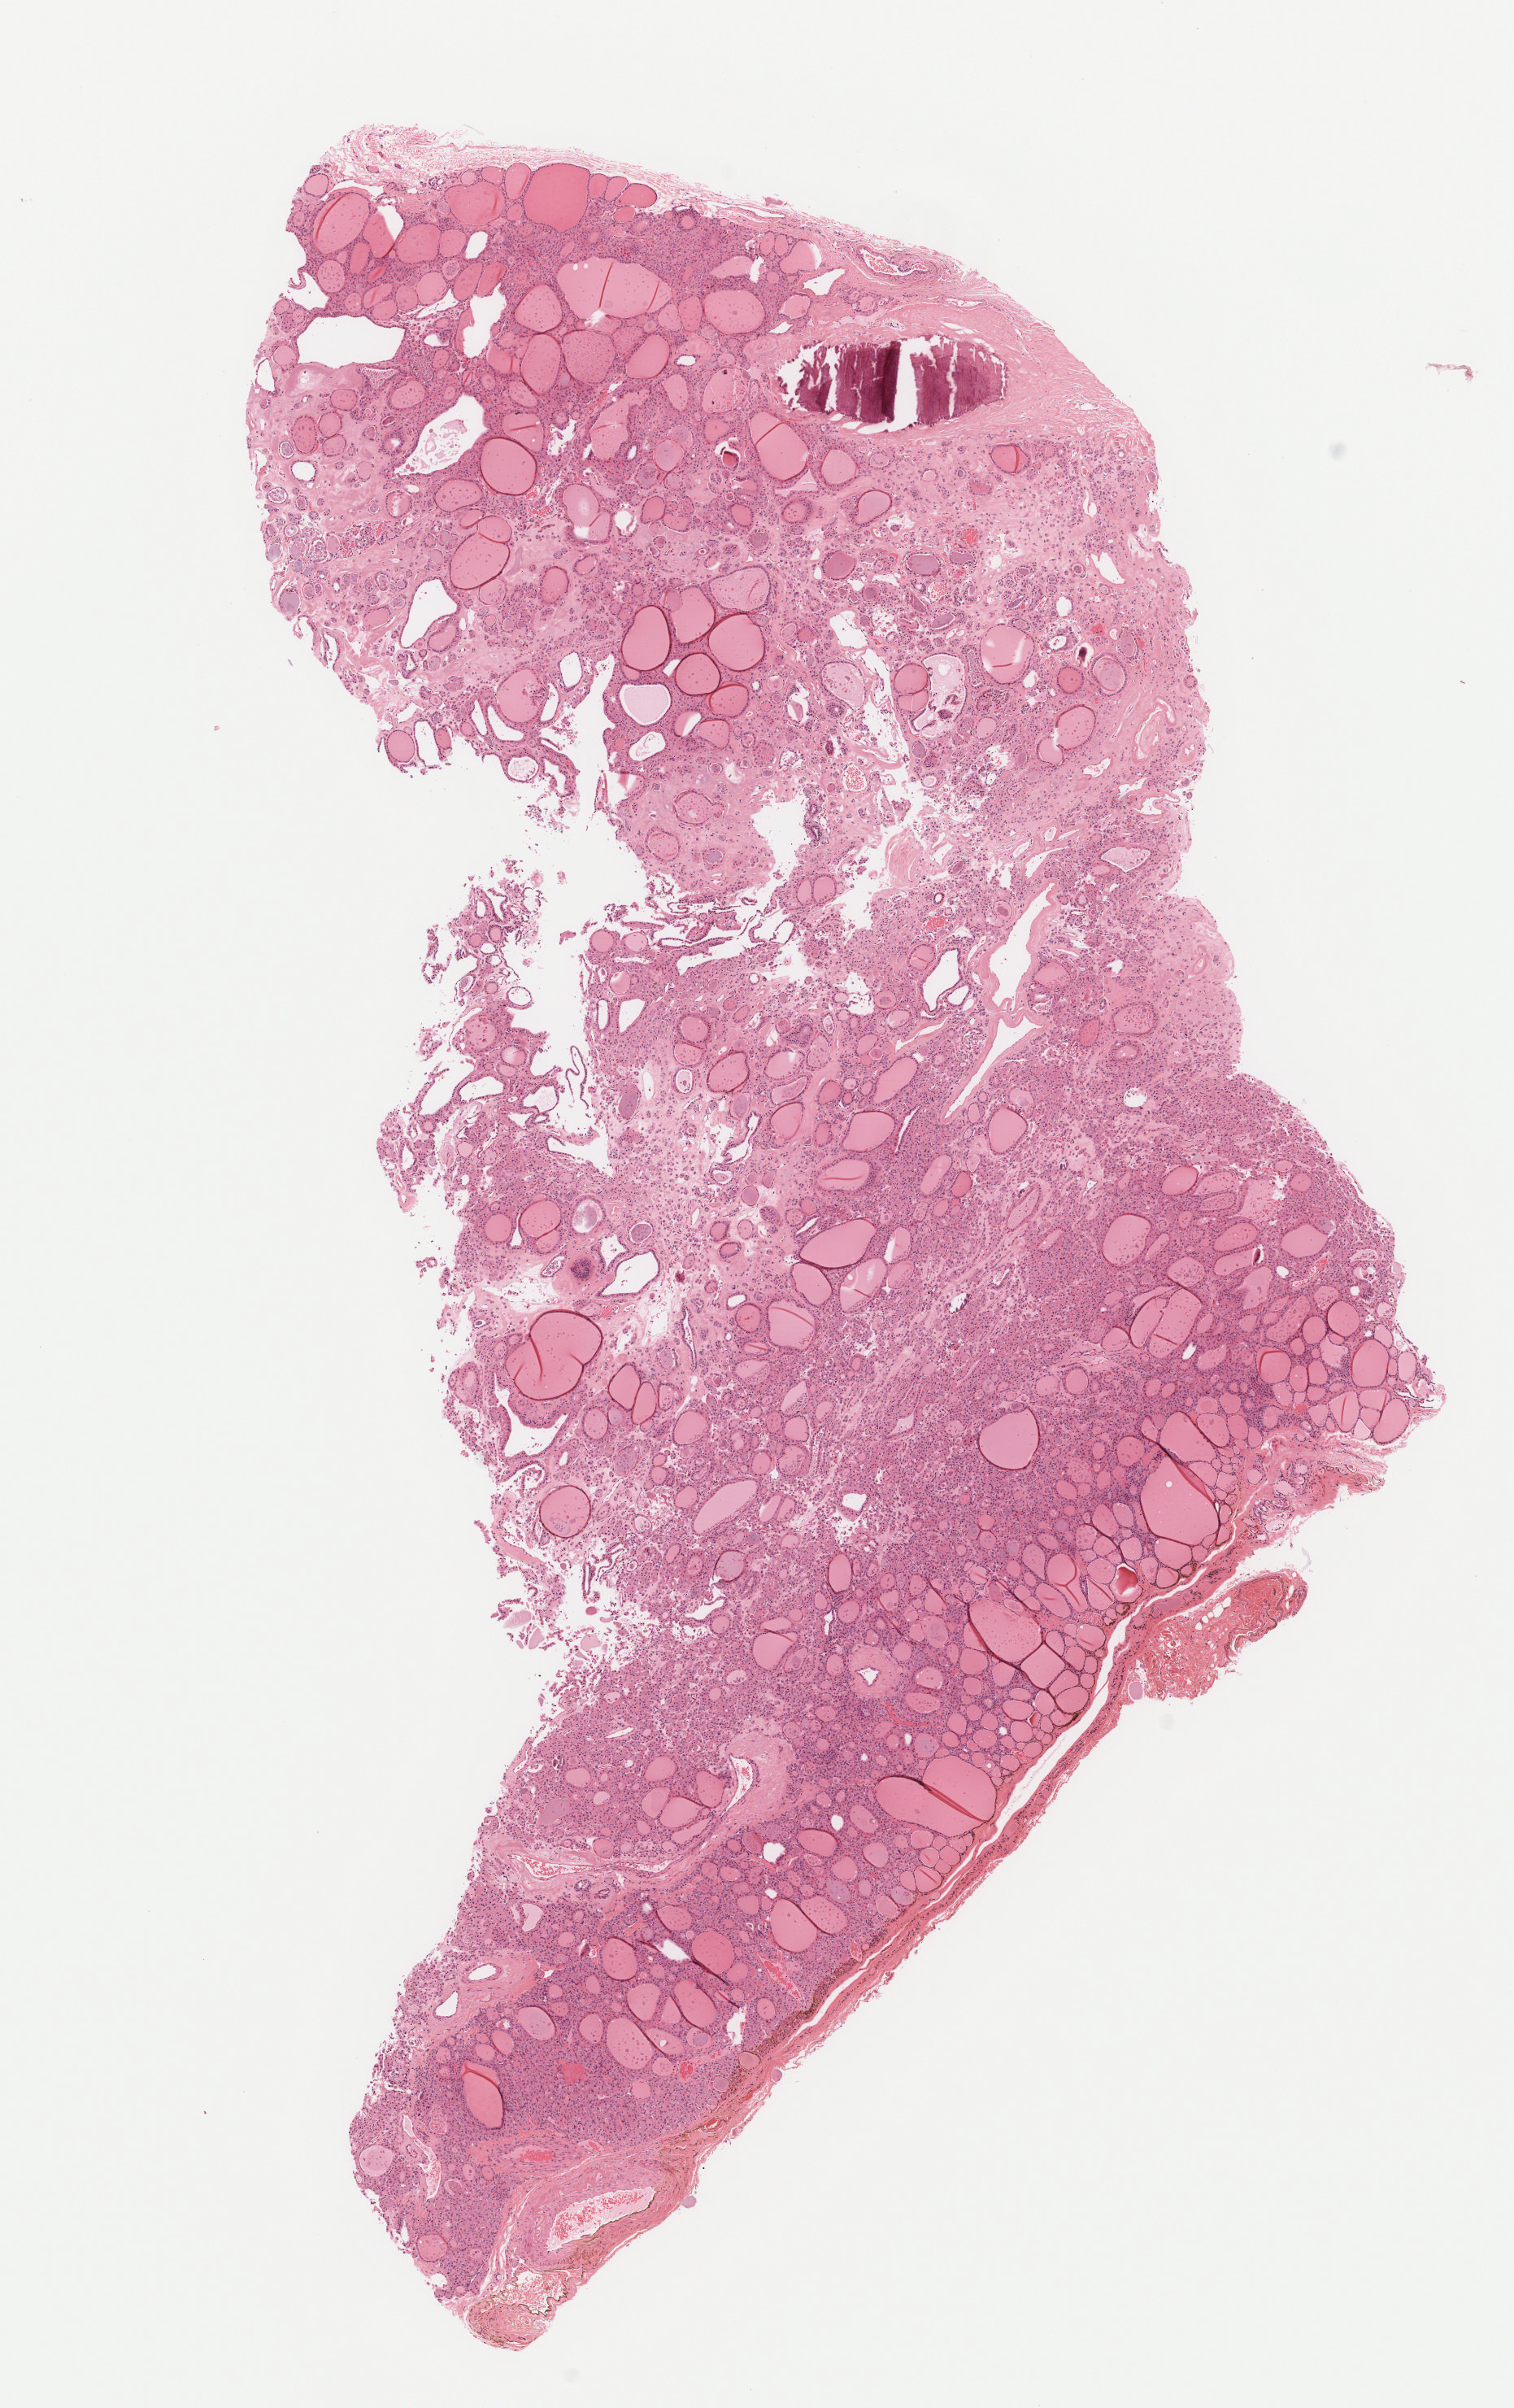
Whole-slide histology image, Hematoxylin and eosin (H&E) stained, whole scanned area (about 7.5 x 11.9 mm) shown as a low-resolution overview; formalin-fixed paraffin-embedded (FFPE) diagnostic section; thyroid, primary tumour sample. Patient: female, age at initial diagnosis 64 years.
• diagnosis: Papillary carcinoma, follicular variant (thyroid gland)
• lymph nodes positive (case pathology): 0 of 1 examined
• TNM: T2 N0 MX
• AJCC pathologic stage: II